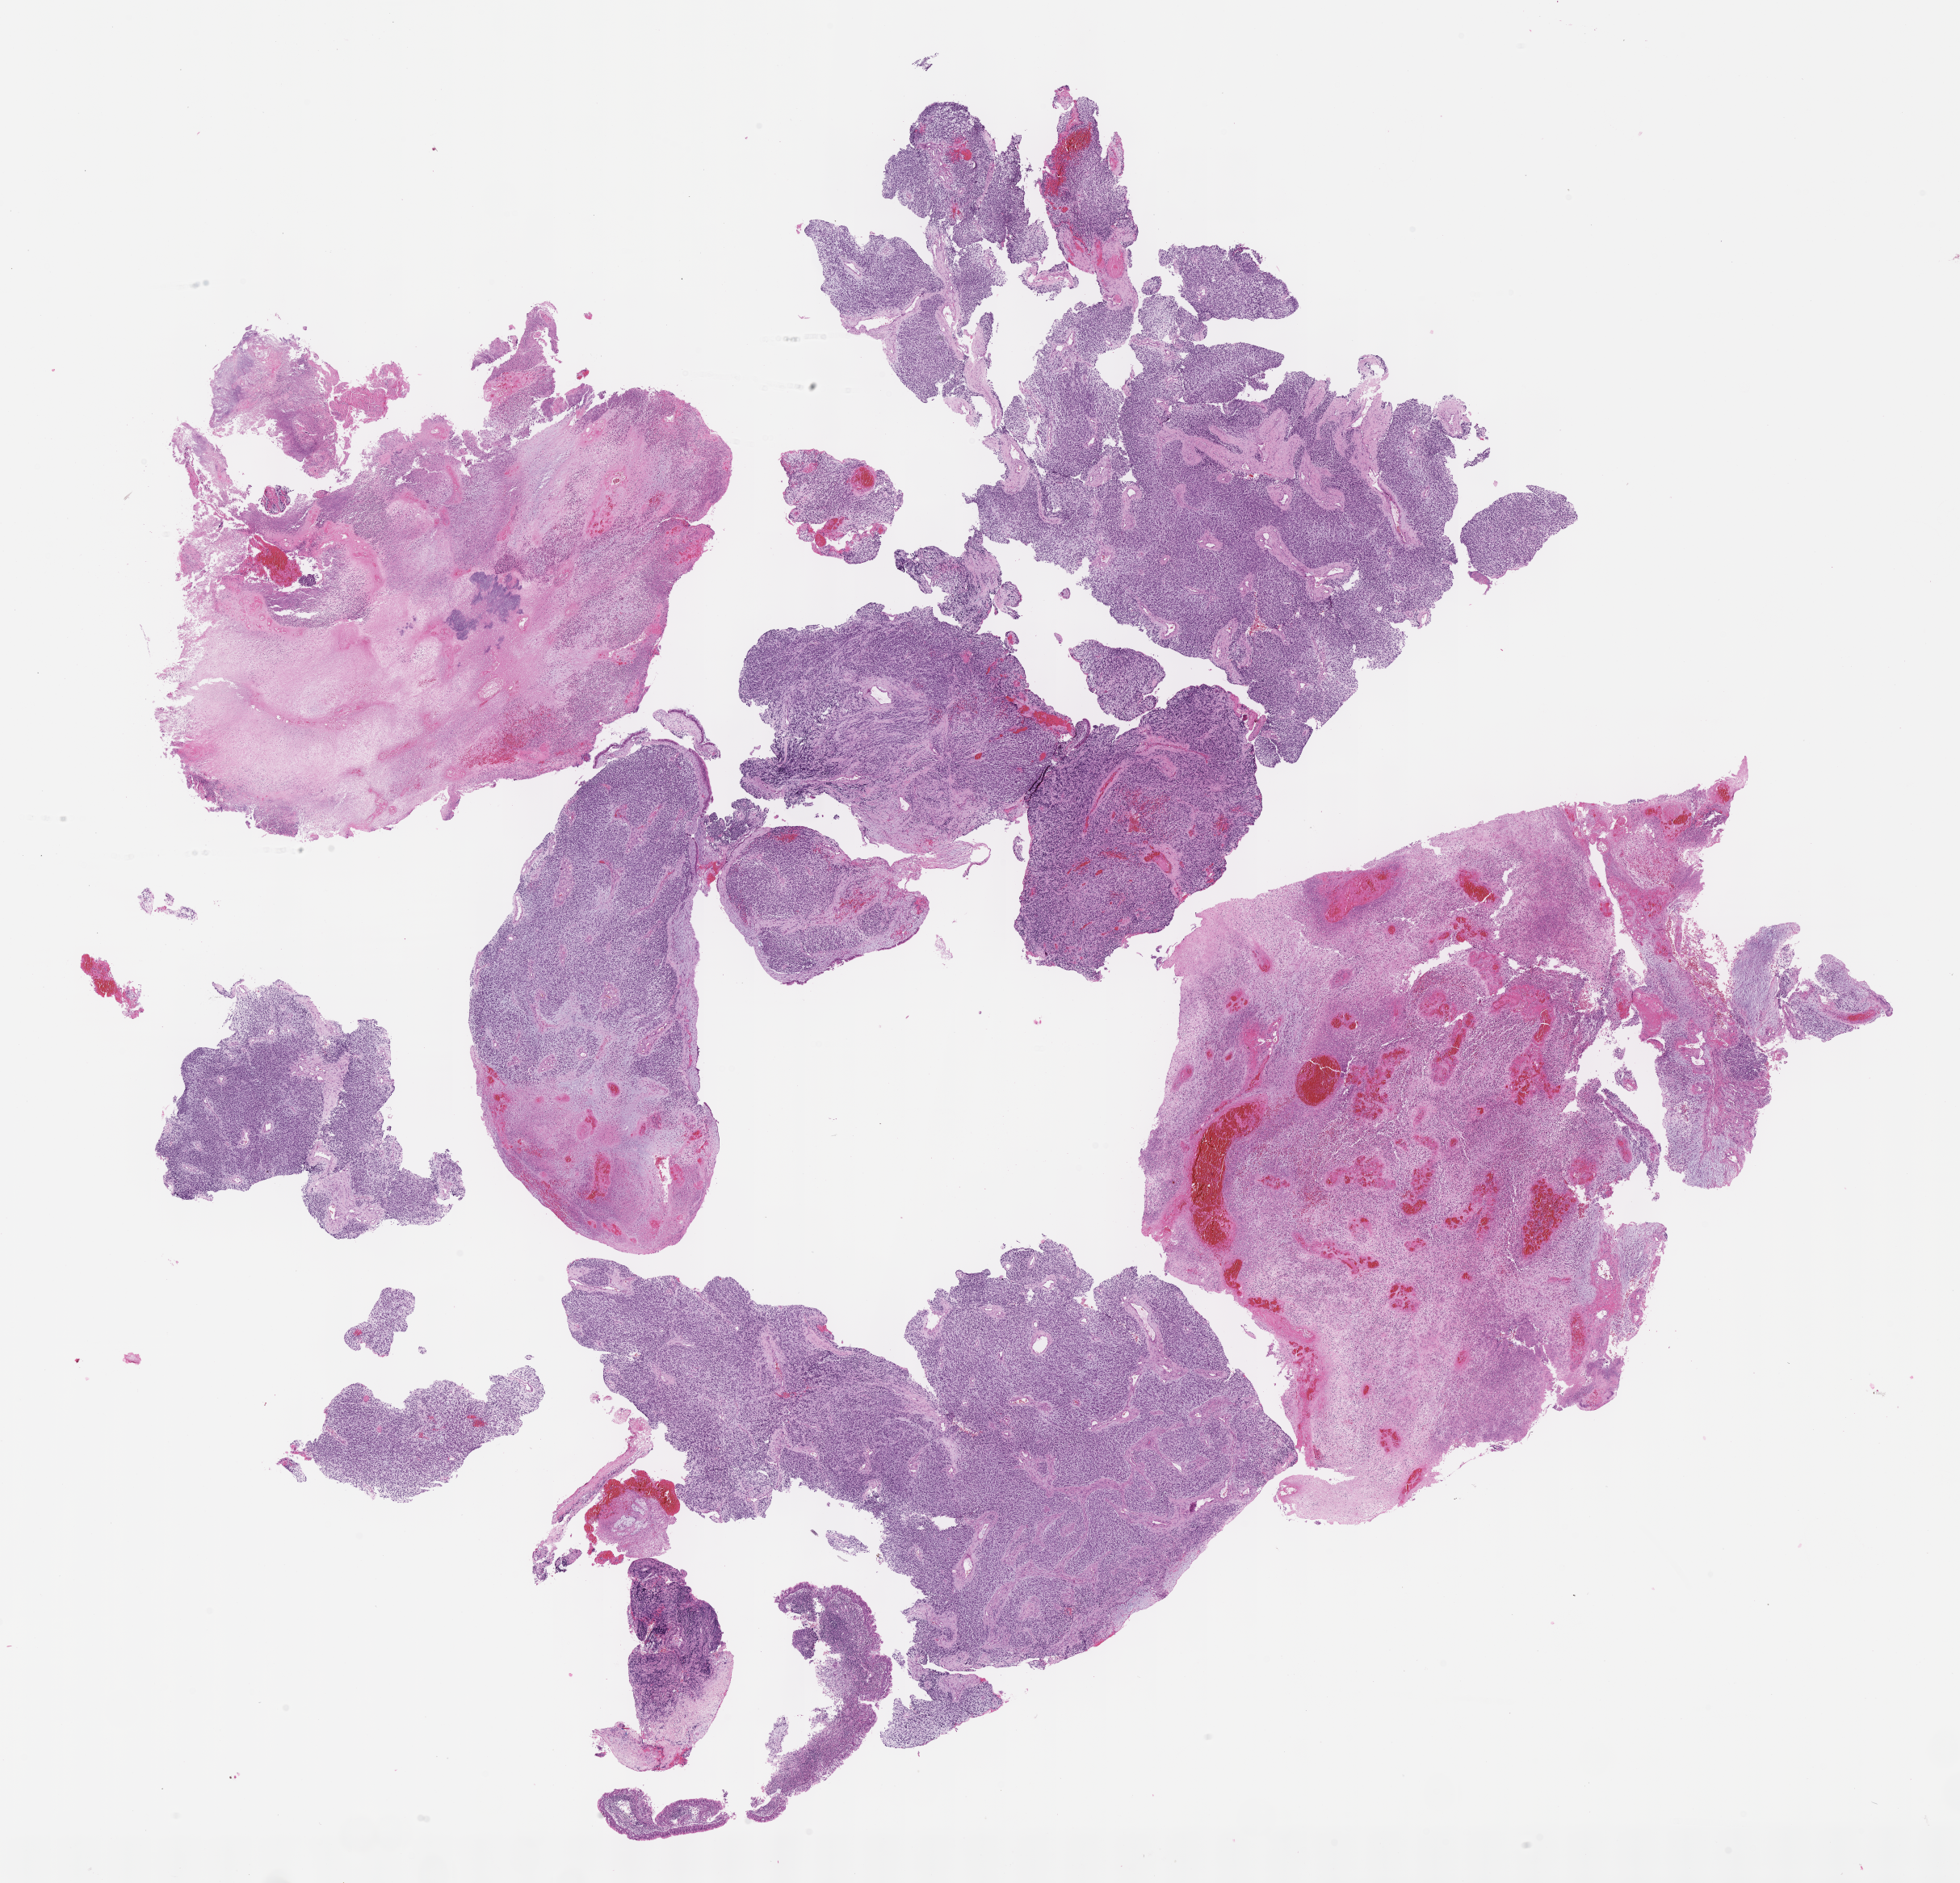
Digitized H&E-stained section of tumor tissue — a low-resolution overview of the entire scanned area, about 19.6 x 18.9 mm. Formalin-fixed, paraffin-embedded (FFPE) tissue. Site: soft tissue, nose-right (nasal cavity). Male patient, age at diagnosis 6.7 years.
Metastatic status at presentation (as recorded): non-metastatic (confirmed). Primary site (case record): nasopharynx (PM). Stage (as recorded): 2. Diagnosis: rhabdomyosarcoma; histological classification: embryonal rhabdomyosarcoma.